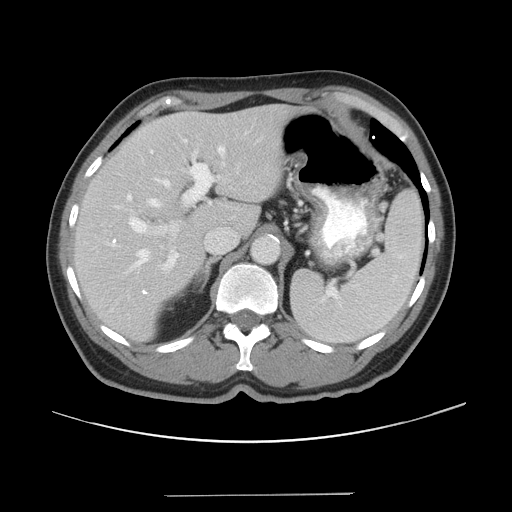
Contrast-enhanced abdominal CT, one axial slice. Slice 28 of 43 in the series (ordered by position). Reconstruction kernel STANDARD. 120 kVp. Soft-tissue window (W 400 / L 40 HU). 5 mm slice thickness. 512 × 512 image matrix. Male patient, age 65 years. From the clinical record (not read from this slice): diagnosis: colorectal cancer liver metastases, imaged before liver resection; multiple liver metastases: no; largest metastasis: 3.8 cm; disease in both lobes: no.
Structures marked on this image (expert manual segmentation):
- hepatic veins: bounding box (x1, y1, x2, y2) in pixels: (136, 163, 225, 265)
- liver: (75, 107, 288, 340)
- planned liver remnant (the part of the liver to remain after resection): (75, 107, 288, 340)
- portal vein (with intrahepatic branches): (127, 144, 269, 272)